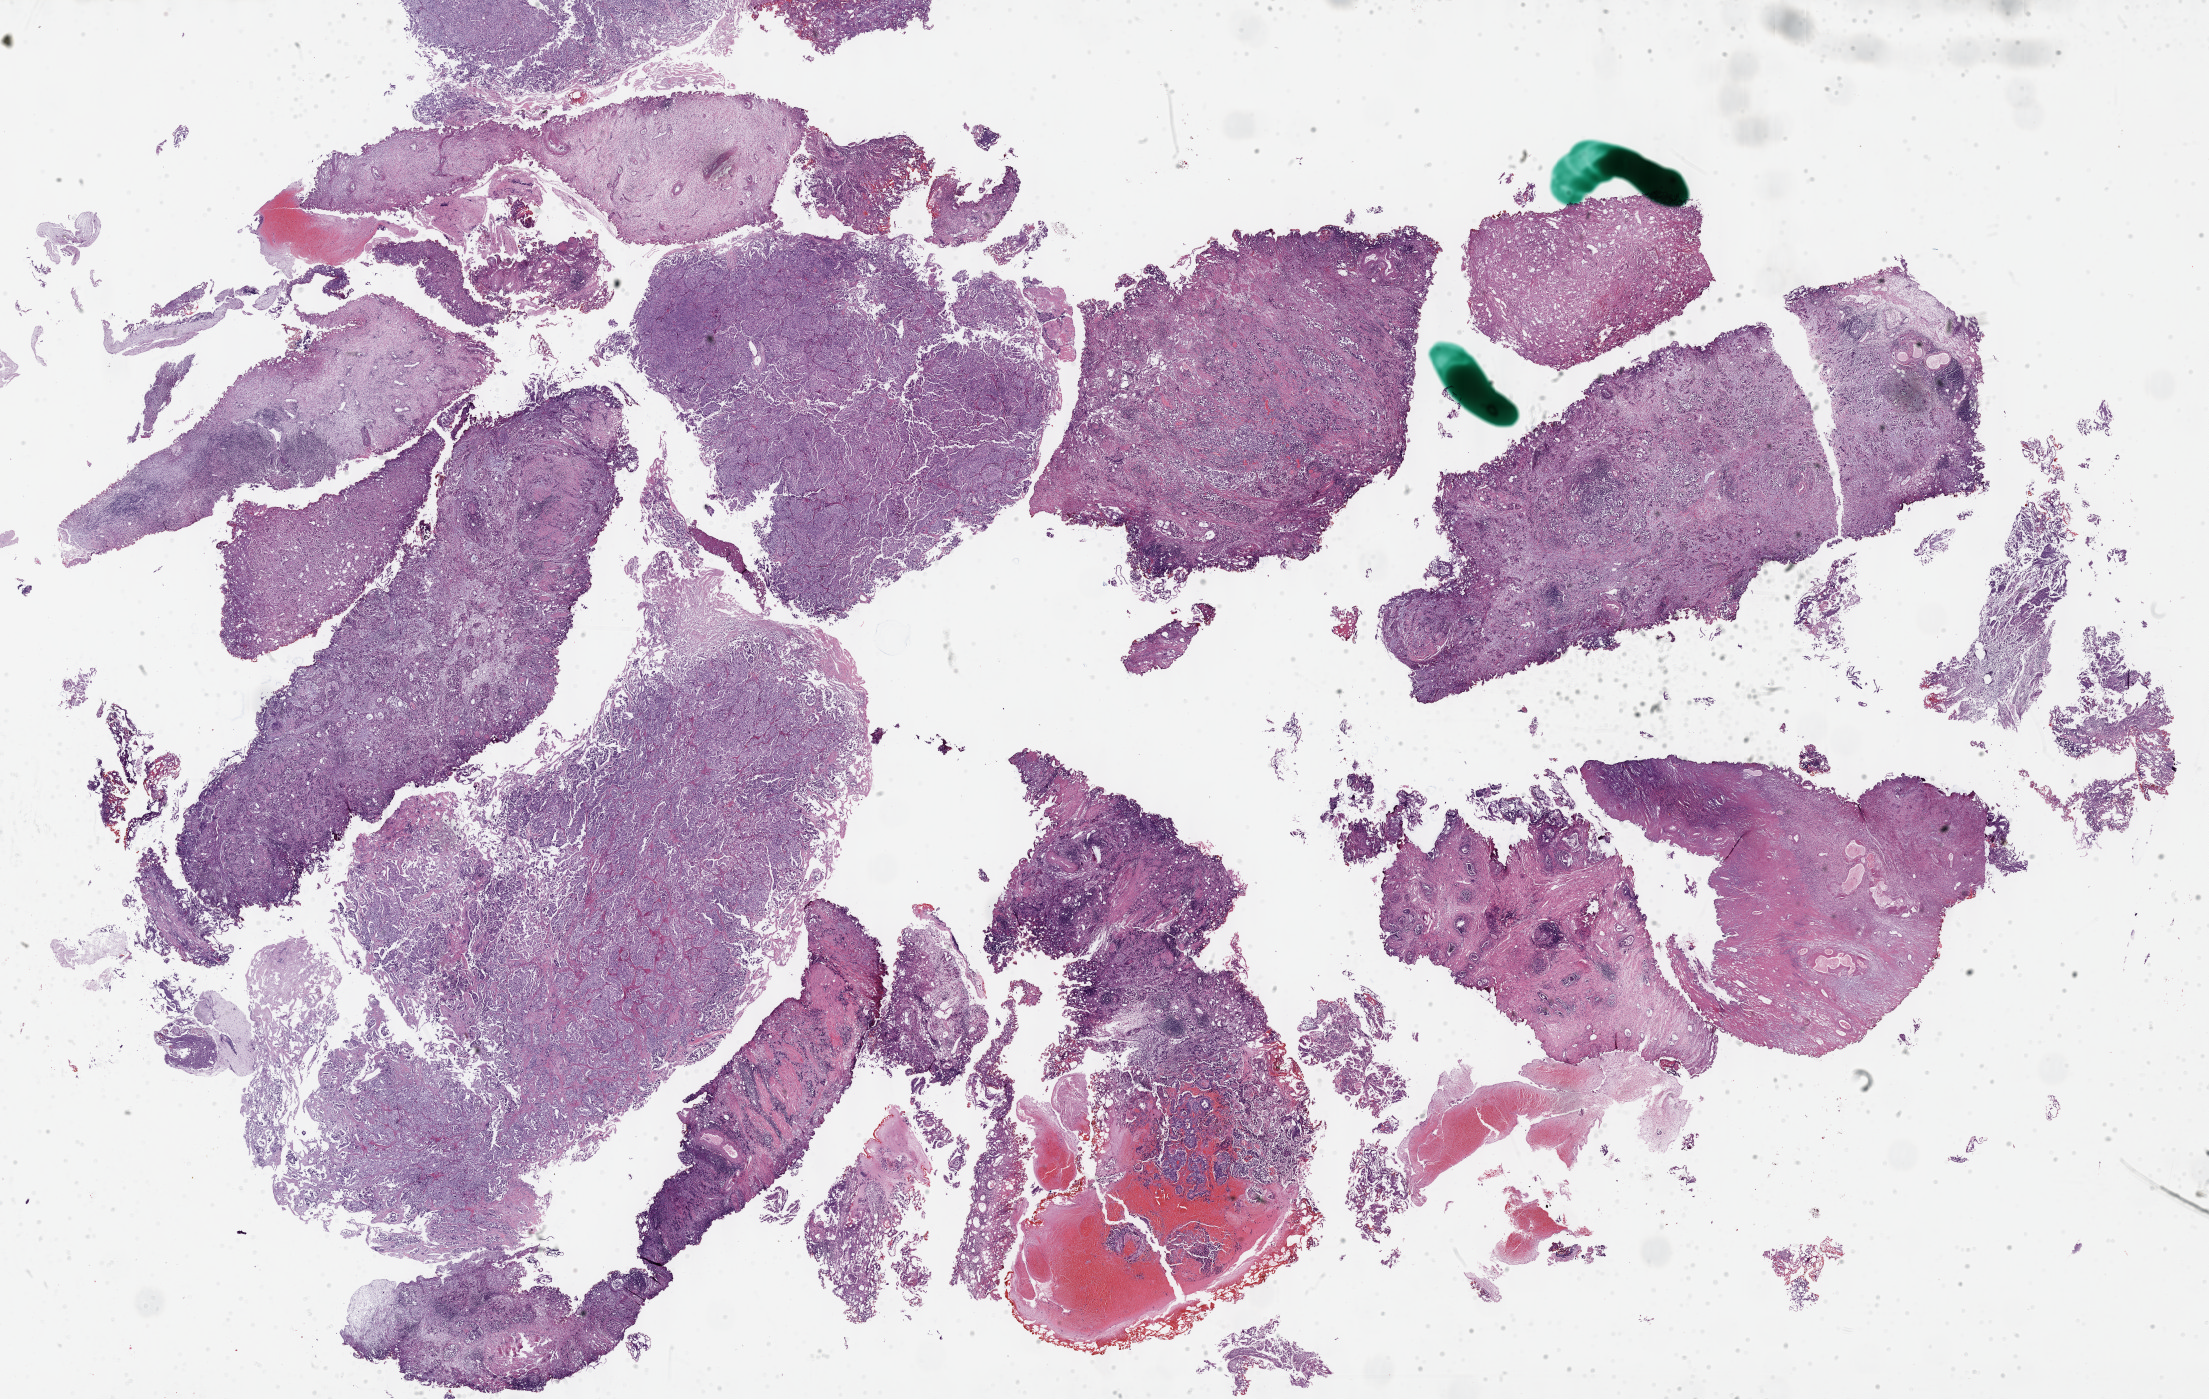
Digitized Hematoxylin and eosin (H&E) stained tissue section (whole slide) — shown as a low-resolution overview of the whole scanned area (about 35.7 x 22.6 mm). Formalin-fixed paraffin-embedded (FFPE) diagnostic section. Bladder, primary tumour sample. Patient: male, age at initial diagnosis 77 years. Histologic grade: high grade.
• histologic diagnosis: Transitional cell carcinoma
• lymph nodes positive (case pathology): 1 of 28 examined
• TNM: T3 N1 M0
• AJCC pathologic stage: IV